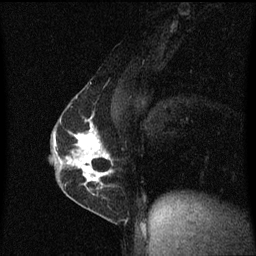
Breast MRI (dynamic contrast-enhanced), one sagittal slice. Position 34 of 60 along the scan axis. Dynamic contrast-enhanced series, image 2 of 3 at this slice position (ordered by acquisition). 1.5 T. TE 4.2 ms, TR 8.4 ms. 256 × 256 image matrix, field of view 200 × 200 mm. Patient: female, 40 years.
Outlined on this slice (semi-automatic segmentation, software-assisted and operator-edited):
- analysis volume of interest (the breast-tissue region the enhancement analysis was run in; not a lesion): bounding box [x1, y1, x2, y2] px = [57, 110, 115, 191]
- tumour enhancement mask (voxels above the 70 % enhancement threshold inside the analysis volume of interest): [66, 116, 111, 189]